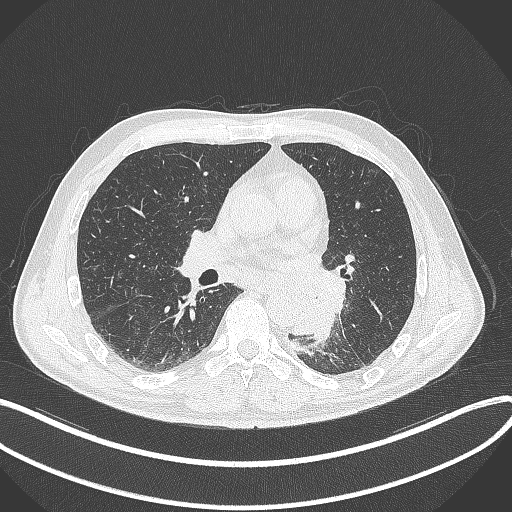
Chest CT, one axial slice; position 172 of 329 along the scan axis; reconstruction kernel B70f; lung window (W 1500 / L -600 HU); 1 mm slice thickness; 512 × 512 image matrix. Patient: male, 59 years. Case-level facts recorded for this patient, not image findings: clinical TNM (as recorded): T2a N2 M0.
Structures marked on this image (rectangle marked by the reading radiologist):
- lung tumour (recorded histology: squamous cell carcinoma): box from (x=283, y=263) to (x=349, y=339) px